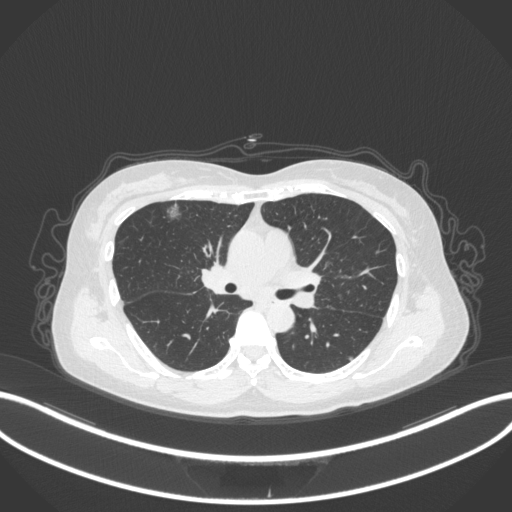
Chest CT, one axial slice. Position 195 of 317 along the scan axis. 120 kVp. Lung window (W 1500 / L -600 HU). 1 mm slice thickness. 512 × 512 image matrix. Female patient, age 61 years. From the clinical record (not read from this slice): clinical TNM (as recorded): T1b N0 M0; histopathological grade: G1.
Outlined on this slice (rectangle marked by the reading radiologist):
- lung tumour (recorded histology: adenocarcinoma): box from (x=165, y=203) to (x=182, y=222) px